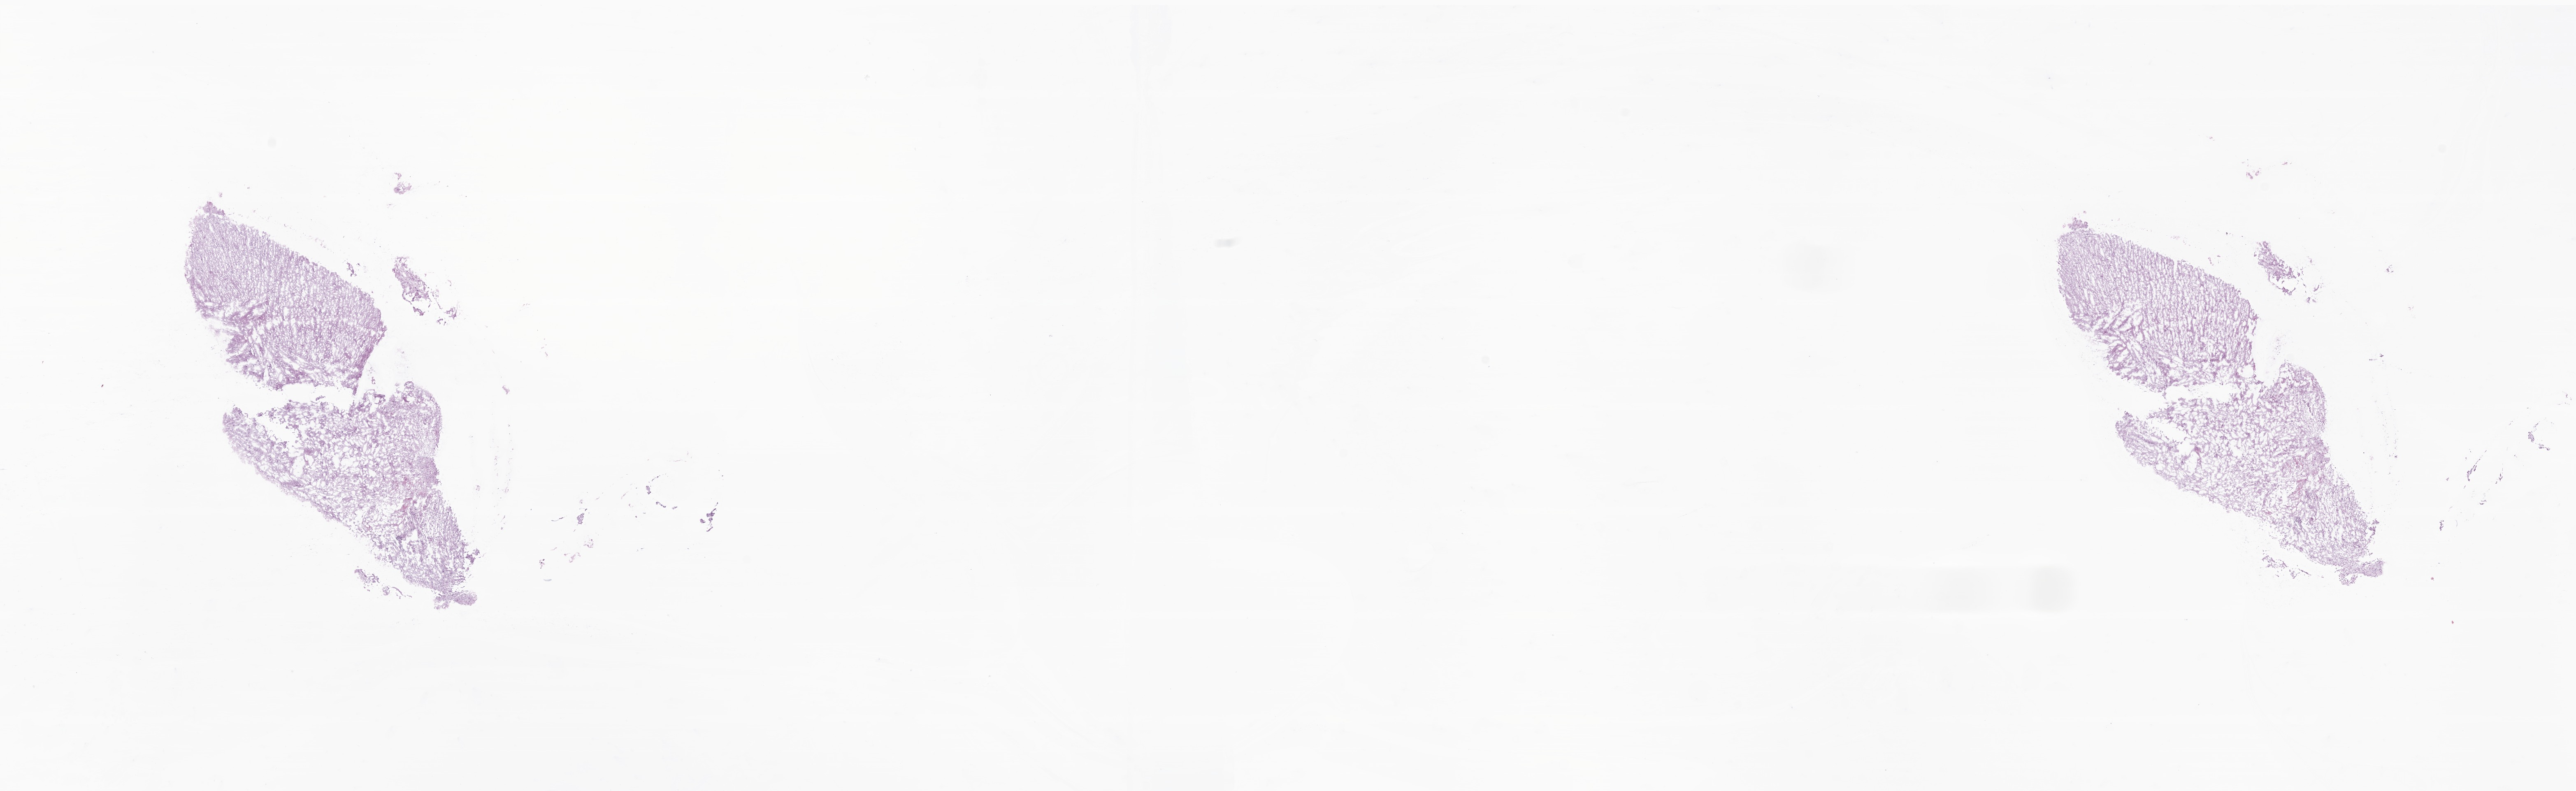
Haematoxylin and eosin whole-slide image of tumor tissue from the parietal lobe, whole scanned area (about 26.4 x 8.1 mm) shown as a low-resolution overview, frozen section (OCT-embedded). Male patient, age 161 months (13 years 5 months).
• diagnosis: Ganglioglioma, NOS